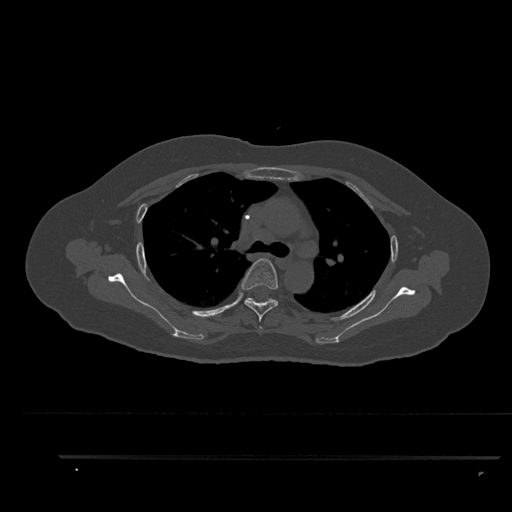
CT including the spine, one axial slice. Position 636 of 797 along the scan axis. Reconstruction kernel Br40s/3. 120 kVp. Bone window (W 1800 / L 400 HU). 512 × 512 image matrix. Female patient, age 44 years. From the clinical record (not read from this slice): primary cancer: renal; vertebrae with lytic lesions (as recorded): L1.
Outlined on this slice (semi-automatic segmentation, software-assisted and operator-edited):
- T3 vertebra: bounding box <260,326,262,329> (left, top, right, bottom; pixels)
- T4 vertebra: <241,258,278,322>
- T5 vertebra: <244,298,251,302>